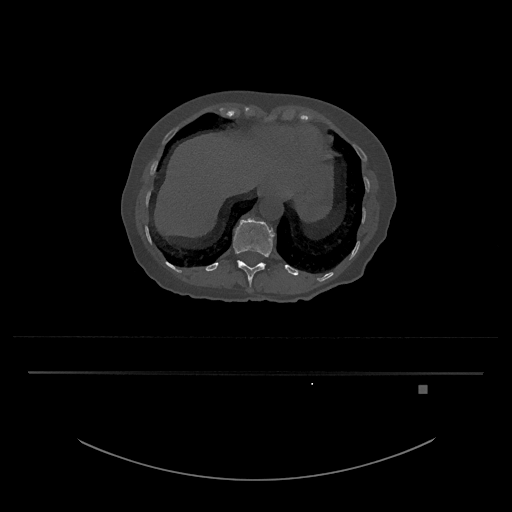
CT including the spine, one axial slice; slice 608 of 797 in the series (ordered by position); 120 kVp; bone window (W 1800 / L 400 HU); 0.5 mm slice thickness; 512 × 512 image matrix. Female patient, age 57 years. Case-level facts recorded for this patient, not image findings: primary cancer: cervical.
Structures marked on this image (semi-automatically segmented with operator editing):
- T12 vertebra: bounding box [x1, y1, x2, y2] px = [233, 218, 275, 289]